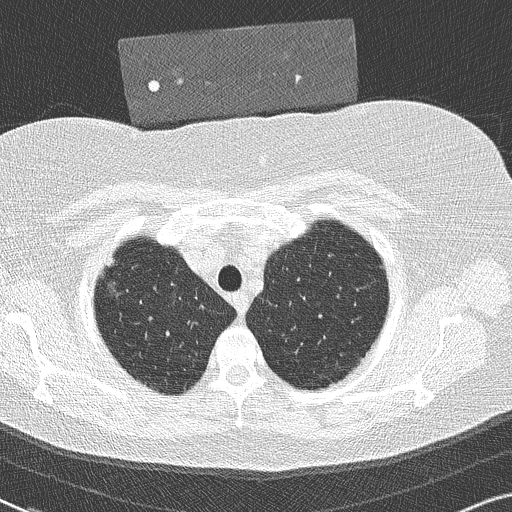
Low-dose screening chest CT, axial slice, baseline screening round, lung window (W 1500 / L -600 HU), 2 mm slice thickness, slice 37 of 306 in the series, 512 × 512 image matrix. Female participant, aged 58 years at enrolment.
Expert reader's lesion annotation, bounding box <95,250,131,296> (left, top, right, bottom; pixels). Screening reader's record for this exam: no non-calcified nodule ≥4 mm recorded. Participant outcome: lung cancer diagnosed 846 days after this screen — bronchiolo-alveolar adenocarcinoma, NOS, right upper lobe, well differentiated (G1), stage IA (AJCC 6th edition), 9 mm at pathology.